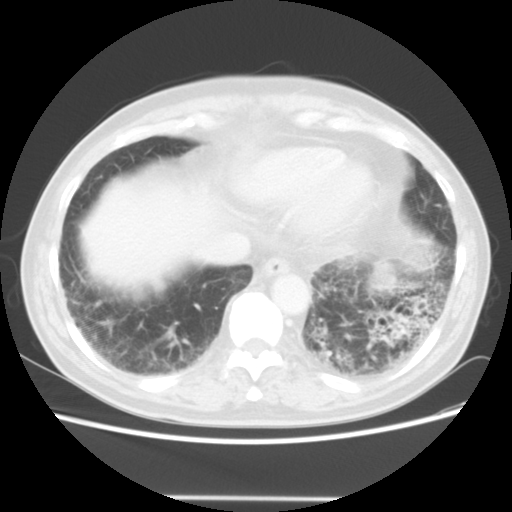
Chest CT, one axial slice. Lung window (W 1500 / L -600 HU). 5 mm slice thickness. 512 × 512 image matrix, field of view 360 × 360 mm. Male patient, age 66 years. From the clinical record (not read from this slice): clinical TNM (as recorded): T4 N3 M0; histopathological grade: G3.
Outlined on this slice (rectangle marked by the reading radiologist):
- lung tumour (recorded histology: small cell carcinoma): bounding box [x1, y1, x2, y2] px = [363, 259, 398, 298]